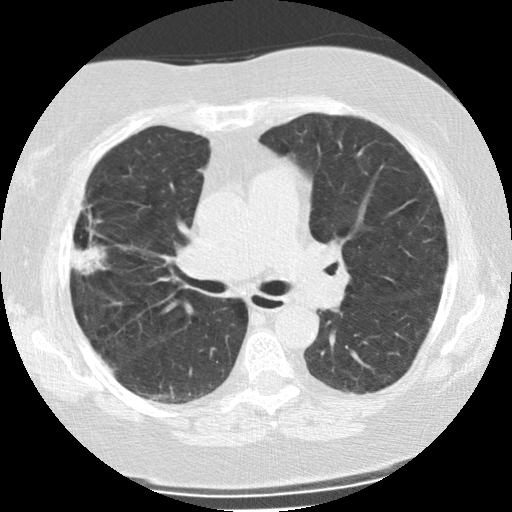
Low-dose screening chest CT, axial slice, second annual screen, lung window (W 1500 / L -600 HU), standard (soft-tissue) reconstruction kernel (STANDARD), slice 88 of 225 in the series, 512 × 512 image matrix. Female participant, aged 73 years at enrolment. Former smoker at enrolment.
Expert-annotated lung lesion, box from (x=56, y=208) to (x=109, y=281) px. The screening reader recorded 2 non-calcified nodules or masses ≥4 mm on this exam (right upper lobe, left upper lobe); which of them this box marks is not recorded. Lung cancer was diagnosed 47 days after this screen: bronchiolo-alveolar adenocarcinoma, NOS, right upper lobe, moderately differentiated (G2), stage IIIB (AJCC 6th edition), 21 mm at pathology.